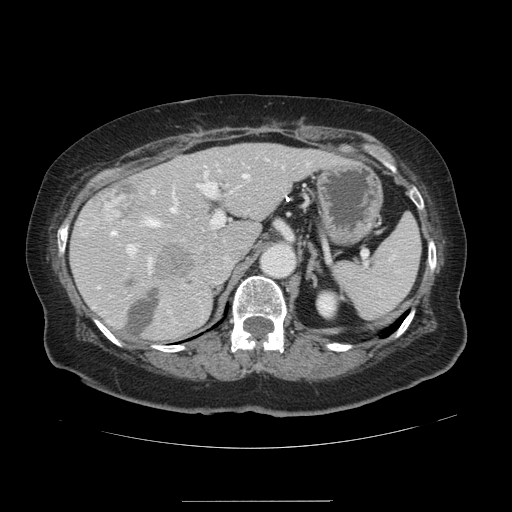
Contrast-enhanced abdominal CT, one axial slice; position 84 of 141 along the scan axis; 120 kVp; intravenous contrast given; soft-tissue window (W 400 / L 40 HU); 2.5 mm slice thickness; 512 × 512 image matrix, field of view 393 × 393 mm. Female patient, age 74 years. Case-level facts recorded for this patient, not image findings: diagnosis: colorectal cancer liver metastases, imaged before liver resection; multiple liver metastases: yes.
Outlined on this slice (expert manual segmentation):
- hepatic veins: bounding box <112,174,247,234> (left, top, right, bottom; pixels)
- liver: <72,144,336,341>
- planned liver remnant (the part of the liver to remain after resection): <72,144,336,340>
- portal vein (with intrahepatic branches): <127,163,308,267>
- liver metastasis: <95,178,147,223>
- liver metastasis: <126,290,160,335>
- liver metastasis: <157,244,194,278>